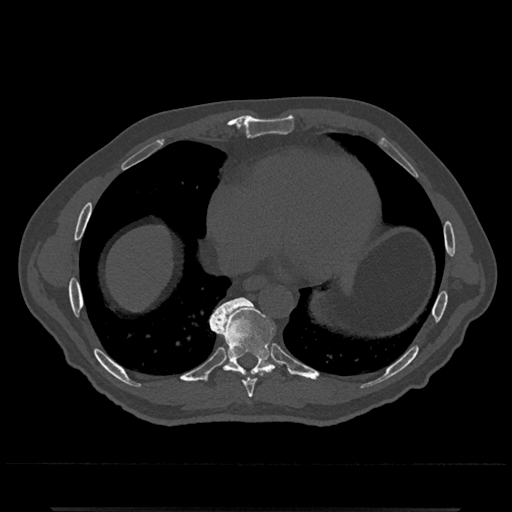
CT including the spine, one axial slice; position 636 of 797 along the scan axis; 120 kVp; bone window (W 1800 / L 400 HU); 512 × 512 image matrix. Patient: male, 67 years. From the clinical record (not read from this slice): primary cancer: prostate.
Outlined on this slice (semi-automatically segmented with operator editing):
- T8 vertebra: bounding box (x1, y1, x2, y2) in pixels: (243, 379, 256, 398)
- T9 vertebra: (210, 298, 278, 375)